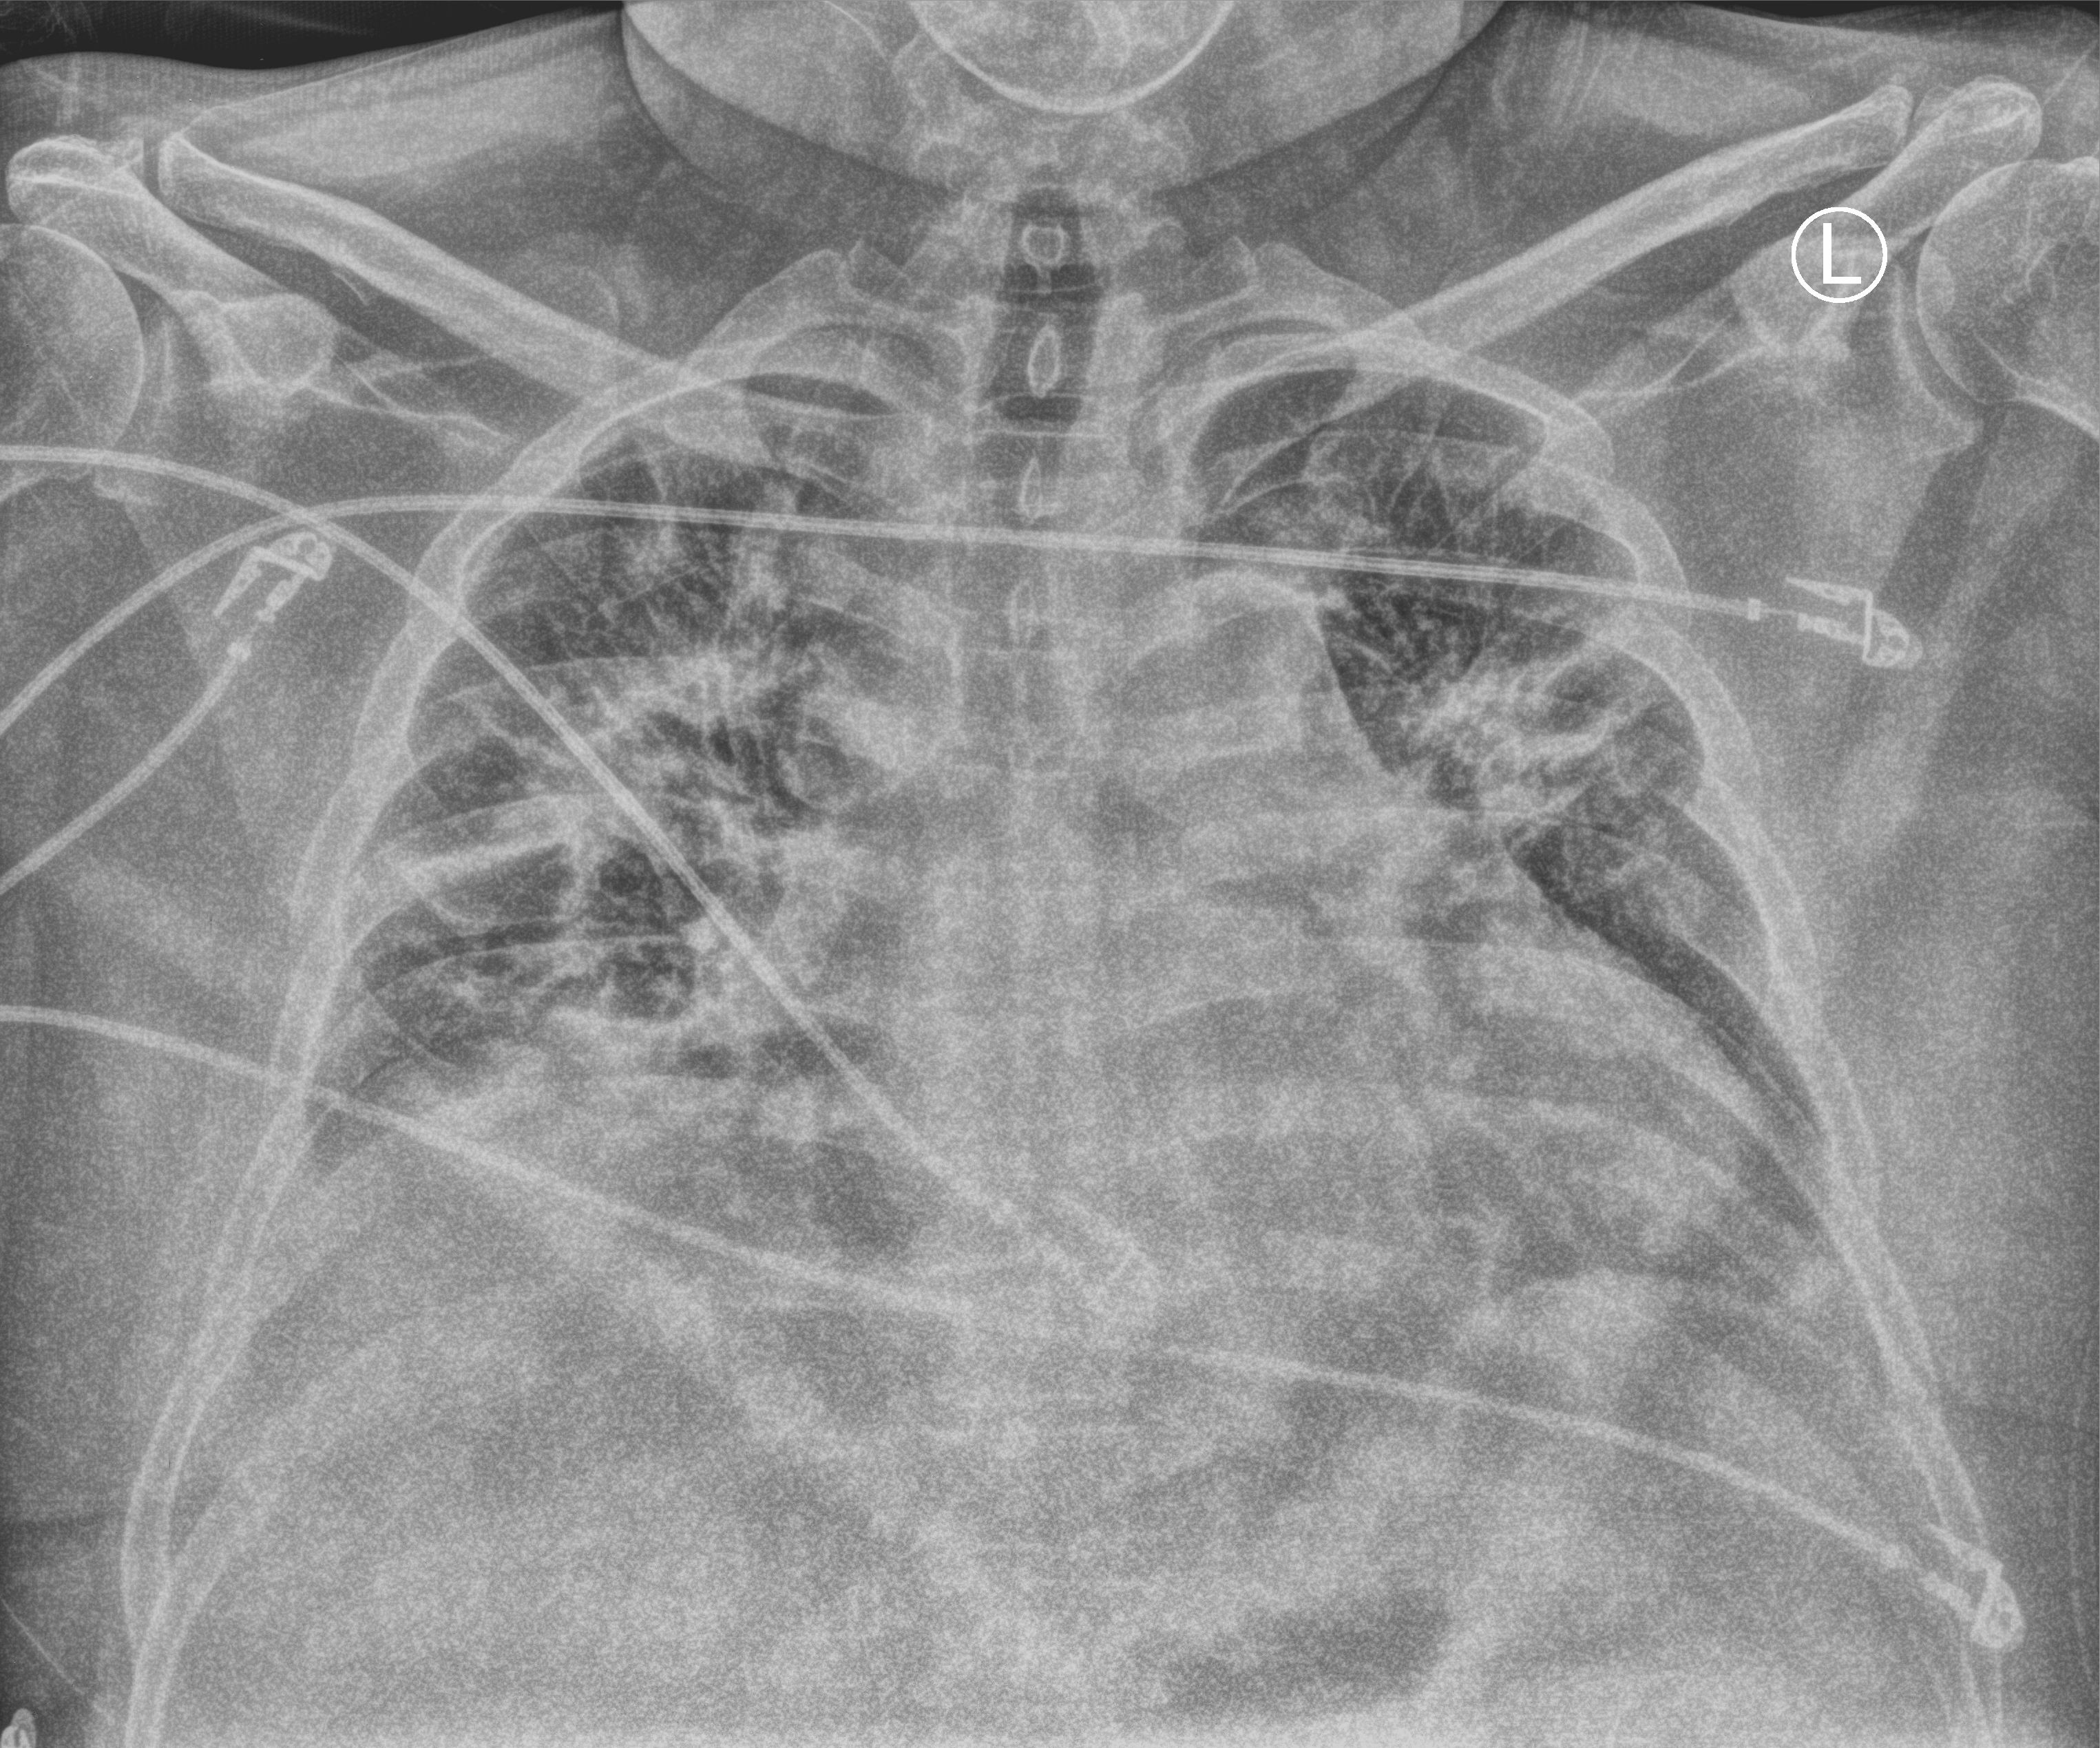
Bedside chest radiograph (computed radiography). Male patient hospitalised with COVID-19, age 18–59 years.
From the hospital-stay record, not from the radiograph (when in the stay this image was taken is not recorded): admitted to intensive care during this hospital stay: no; mechanically ventilated during this hospital stay: no.